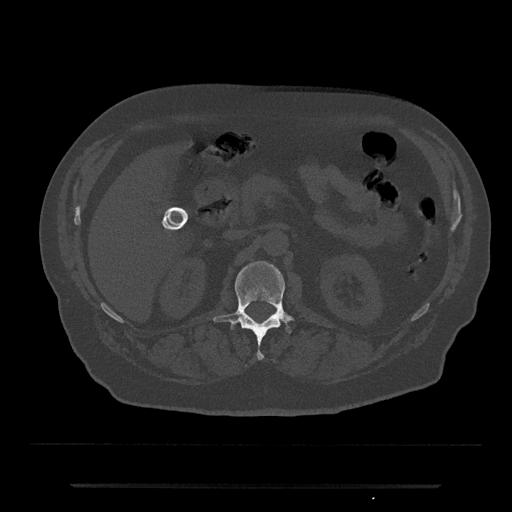
CT including the spine, one axial slice. Position 533 of 797 along the scan axis. Reconstruction kernel Br40s/3. 120 kVp. Bone window (W 1800 / L 400 HU). 0.5 mm slice thickness. 512 × 512 image matrix. Male patient, age 80 years. From the clinical record (not read from this slice): primary cancer: prostate; vertebrae with lytic lesions (as recorded): L1, T11.
Annotated regions visible in this slice (semi-automatically segmented with operator editing):
- L1 vertebra: bounding box [x1, y1, x2, y2] px = [214, 261, 291, 360]